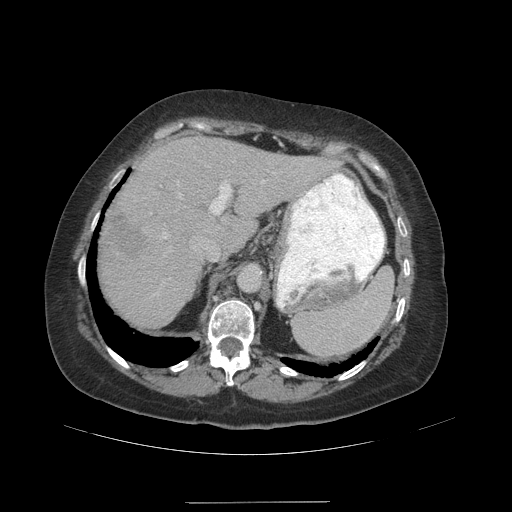
Contrast-enhanced abdominal CT (liver protocol), one axial slice. Position 71 of 99 along the scan axis. Reconstruction kernel STANDARD. 140 kVp. Soft-tissue window (W 400 / L 40 HU). 2.5 mm slice thickness. 512 × 512 image matrix, field of view 440 × 440 mm. From the clinical record (not read from this slice): diagnosis: hepatocellular carcinoma (patient treated with transarterial chemoembolisation; whether this scan precedes or follows treatment is not stated here); TNM stage (as recorded): Stage-IVA; Child-Pugh class: A; tumour nodularity: multinodular.
Annotated regions visible in this slice (semi-automatically segmented with operator editing):
- liver parenchyma outside the tumour (the mass and vessels are separate outlines, so this box may not span the whole liver): bounding box [x1, y1, x2, y2] px = [98, 136, 332, 326]
- mass: [105, 215, 148, 259]
- liver vessels: [163, 180, 266, 249]